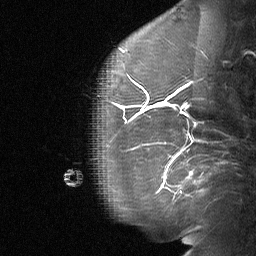
Breast MRI (dynamic contrast-enhanced), one sagittal slice; position 18 of 64 along the scan axis; dynamic contrast-enhanced study with each time point stored as its own series, time point 2 of 3 at this slice position (early post-contrast, ordered by acquisition time); 1.5 T; TE 4.8 ms, TR 27 ms; 2 mm slice thickness; 256 × 256 image matrix. Patient: female, 60 years. From the clinical record (not read from this slice): setting: breast cancer imaged before/during neoadjuvant chemotherapy; receptor status: HR-positive, HER2-negative.
Structures marked on this image (semi-automatically segmented with operator editing):
- analysis volume of interest (the breast-tissue region the enhancement analysis was run in; not a lesion): bounding box (x1, y1, x2, y2) in pixels: (97, 56, 139, 104)
- tumour enhancement mask (voxels above the 90 % enhancement threshold inside the analysis volume of interest): (134, 82, 139, 86)